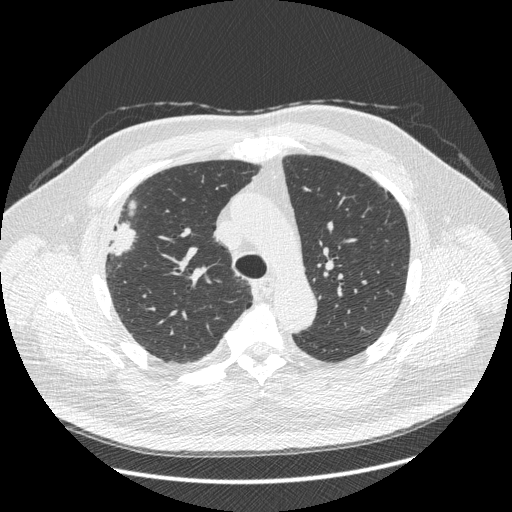
Low-dose screening chest CT, one axial slice. Slice 304 of 426 in the series (ordered by position). Reconstruction kernel STANDARD. 120 kVp. Lung window (W 1500 / L -600 HU). 1.25 mm slice thickness. 512 × 512 image matrix, field of view 400 × 400 mm.
Outlined on this slice (manually delineated by an expert):
- lesion 1 (tumor, upper lobe of right lung): box from (x=109, y=223) to (x=135, y=255) px